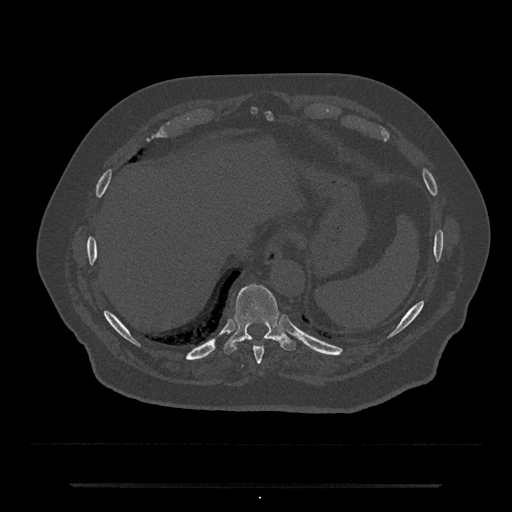
CT including the spine, one axial slice; slice 724 of 797 in the series (ordered by position); reconstruction kernel Br40s/3; bone window (W 1800 / L 400 HU); 512 × 512 image matrix. Male patient, age 80 years. Case-level facts recorded for this patient, not image findings: primary cancer: prostate.
Outlined on this slice (semi-automatically segmented with operator editing):
- T10 vertebra: bounding box [x1, y1, x2, y2] px = [223, 284, 296, 354]
- T9 vertebra: [253, 346, 264, 365]